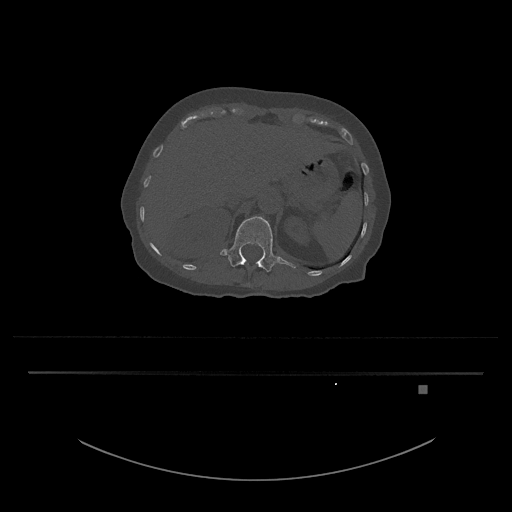
CT including the spine, one axial slice; slice 562 of 797 in the series (ordered by position); 120 kVp; bone window (W 1800 / L 400 HU); 0.5 mm slice thickness; 512 × 512 image matrix, field of view 500 × 500 mm. Female patient, age 57 years. Case-level facts recorded for this patient, not image findings: primary cancer: cervical.
Outlined on this slice (semi-automatic segmentation, software-assisted and operator-edited):
- L1 vertebra: bounding box <220,216,296,272> (left, top, right, bottom; pixels)